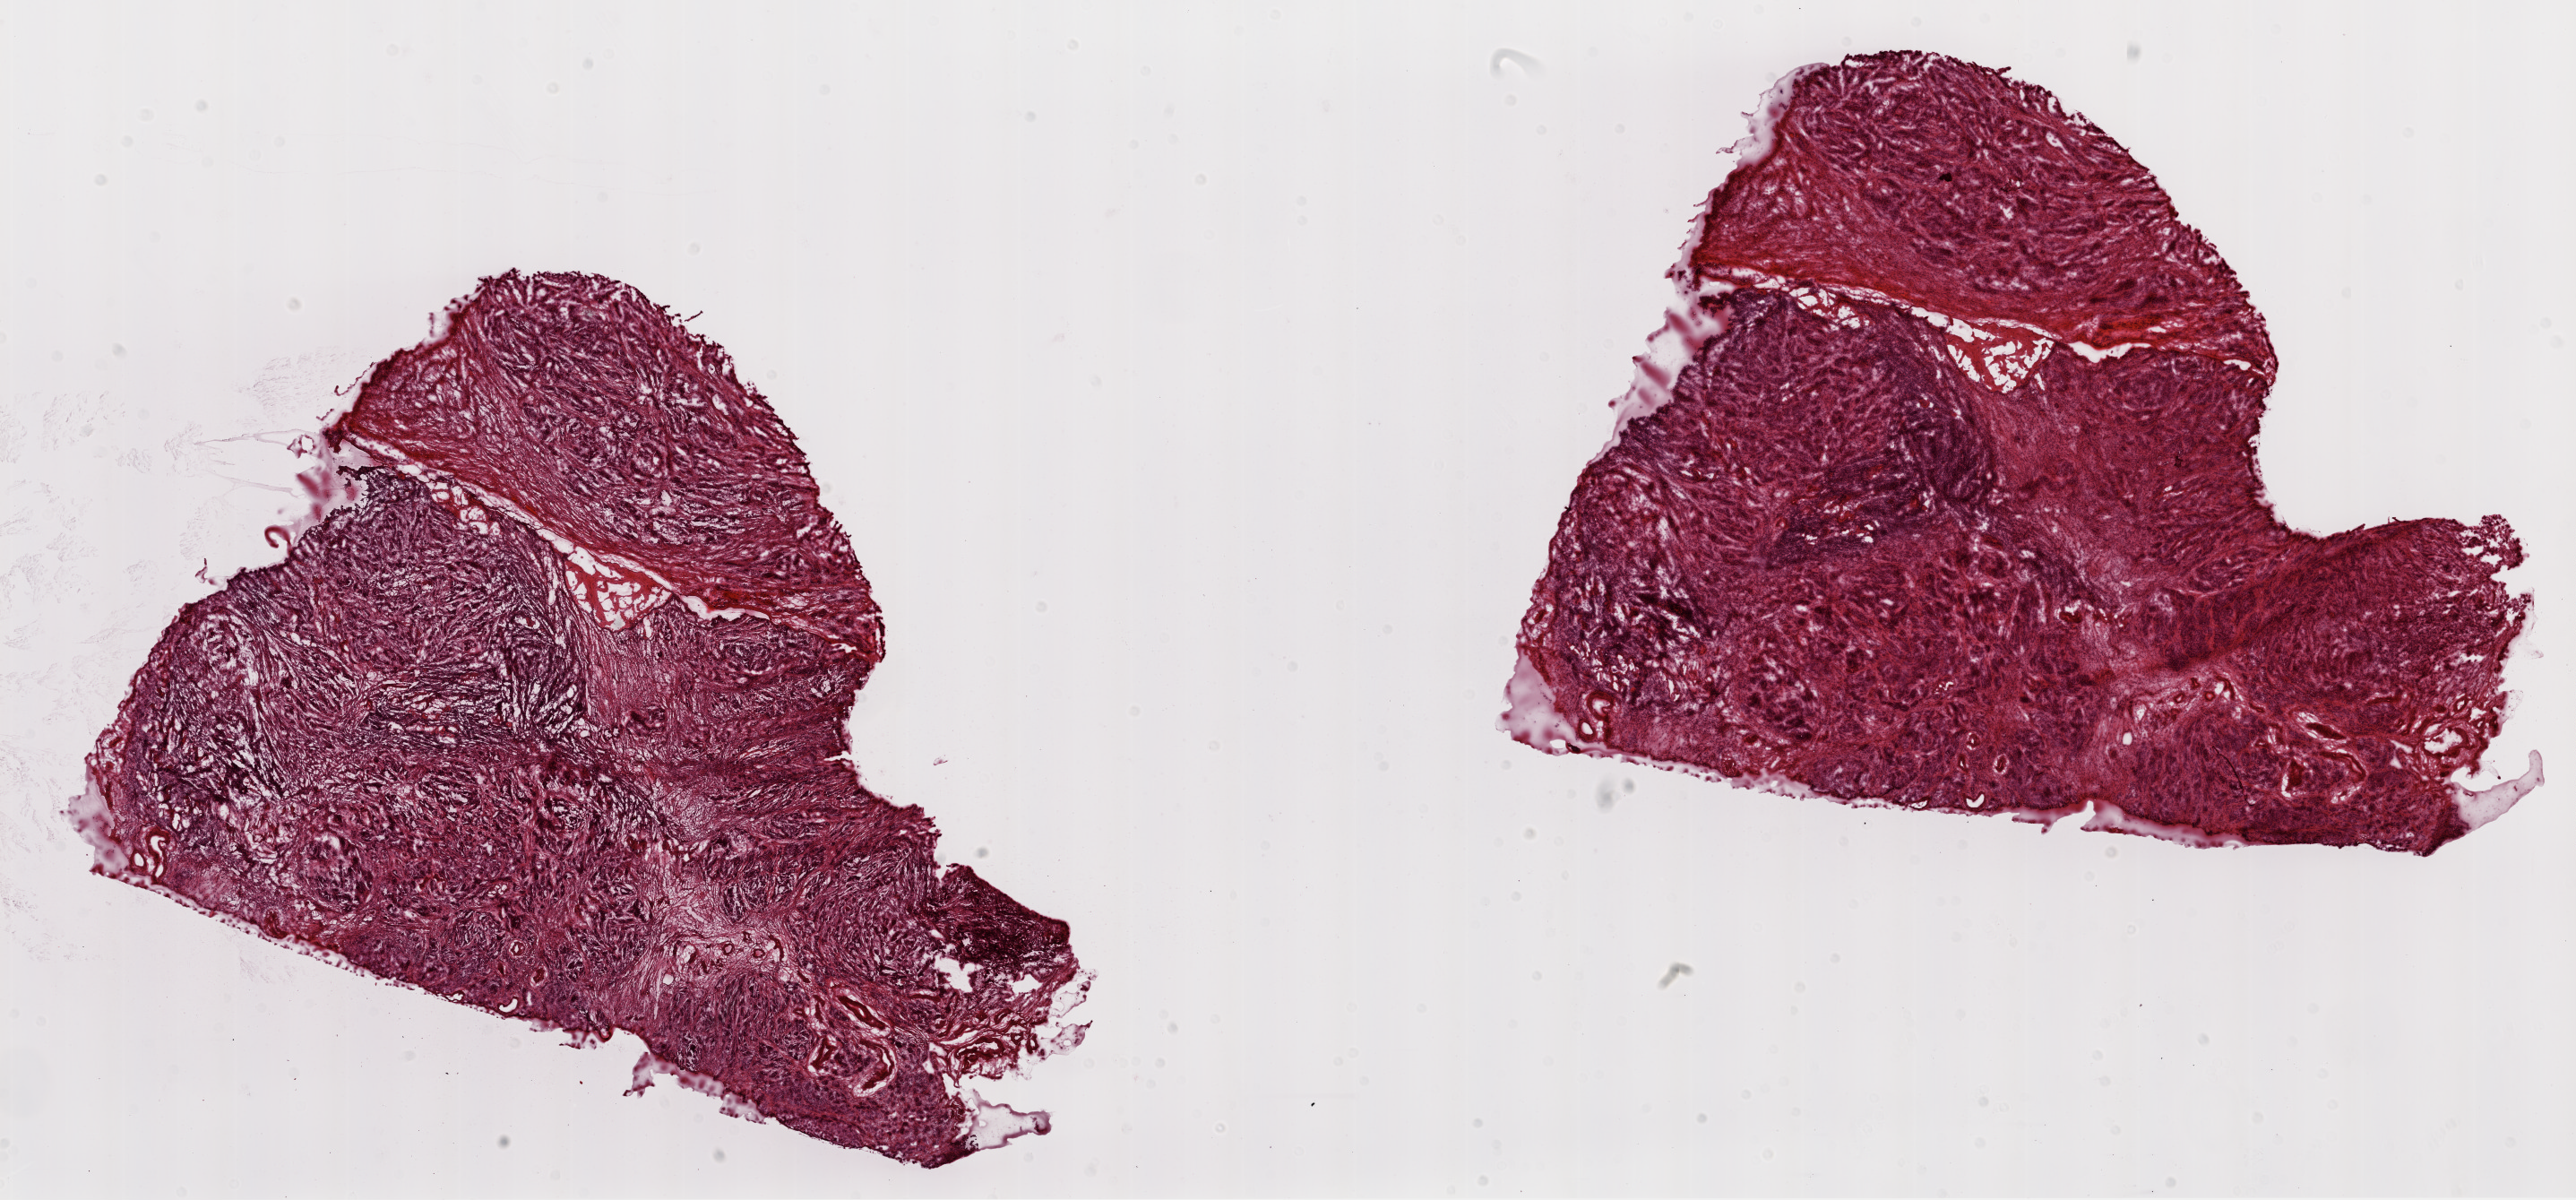
Whole-slide histology image, H&E-stained, a low-resolution overview of the entire scanned area, about 23.1 x 10.7 mm (acquisition: 20x scan); frozen section; primary tumour sample from the ovary. Female patient; age at initial diagnosis 51 years. Histologic grade: G3 (poorly differentiated). Composition of this section per pathologist review: tumour cells 70%, tumour nuclei 70%, normal cells 0%, stromal cells 15%, necrosis 15%. Inflammatory infiltration, as recorded: lymphocyte infiltration 0%, monocyte infiltration 0%, neutrophil infiltration 10%.
Histologic diagnosis: Serous cystadenocarcinoma, NOS. Laterality: bilateral. FIGO stage: IIIC.